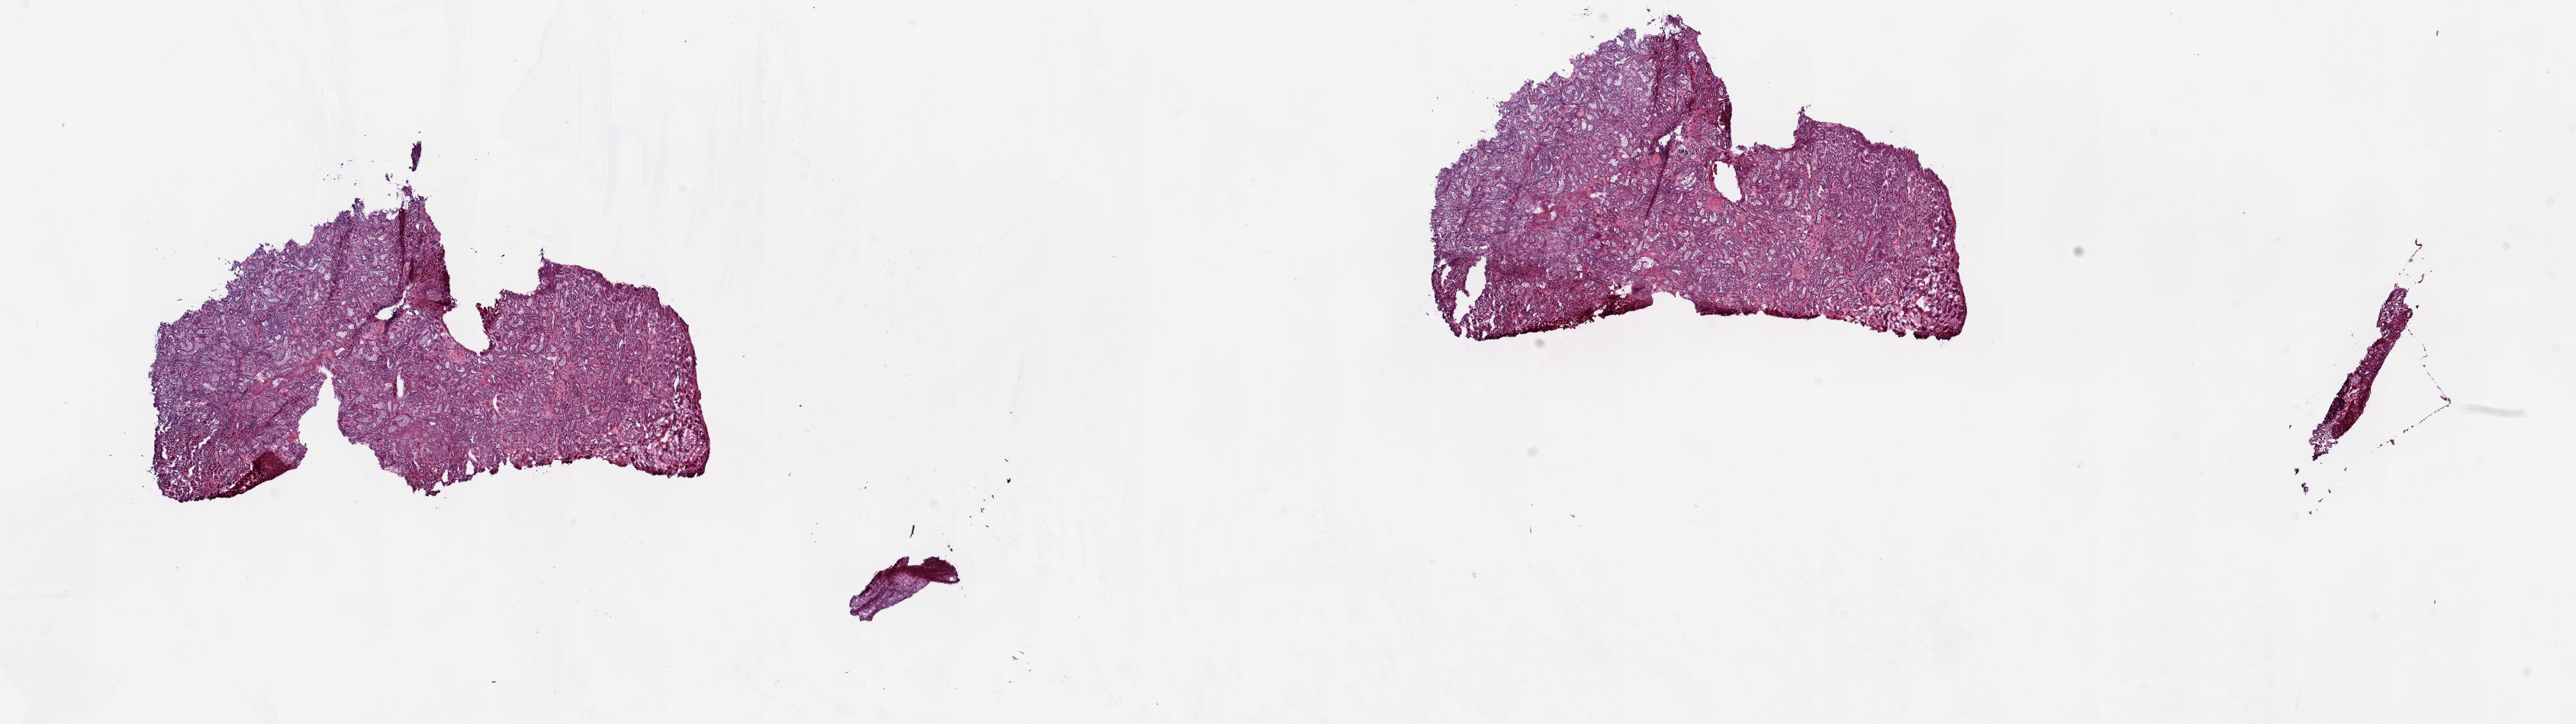
H&E whole-slide image, shown as a low-resolution overview of the whole scanned area (about 26.8 x 7.5 mm); frozen section from the top of the tissue portion; kidney, solid tissue normal (non-tumour tissue) sample. Patient: male, age at initial diagnosis 58 years. Composition of this section per pathologist review: tumour cells 0%, tumour nuclei 0%, normal cells 65%, stromal cells 35%, necrosis 0%. Infiltration values recorded for this section: lymphocyte infiltration 2%, monocyte infiltration 1%, neutrophil infiltration 0%.
This section: solid tissue normal (non-tumour) sample from the same patient. Patient diagnosis: Papillary adenocarcinoma, NOS.